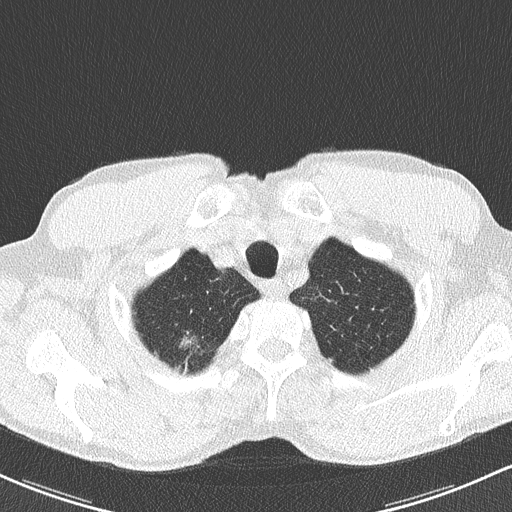
Low-dose screening chest CT, axial slice. Baseline annual screen. Lung window (W 1500 / L -600 HU). Lung (sharp) reconstruction kernel (B50f). Male participant, aged 62 years at enrolment. Former smoker at enrolment.
Lesion marked by an expert reader, bounding box [x1, y1, x2, y2] px = [165, 327, 209, 367]. Reader record for this screening exam (exam-level; its link to the box is not recorded): non-calcified nodule or mass ≥4 mm, right upper lobe, 12 × 9 mm, spiculated (stellate) margins, soft tissue attenuation. Official screen result: positive, change unspecified: nodule(s) >= 4 mm or enlarging nodule(s), mass(es), or other non-specific abnormalities suspicious for lung cancer.